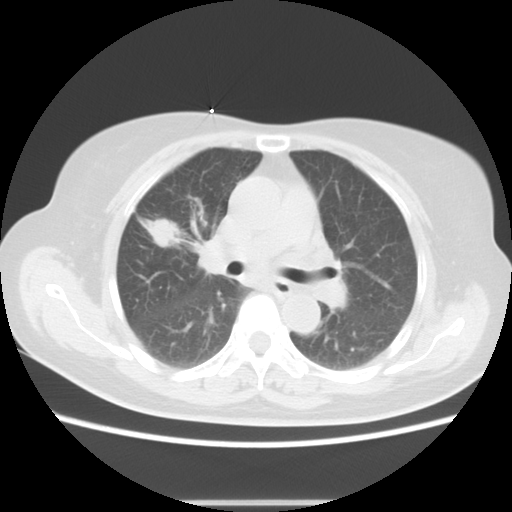
Chest CT, one axial slice; slice 7 of 17 in the series (ordered by position); lung window (W 1500 / L -600 HU); 512 × 512 image matrix. Female patient, age 57 years. Case-level facts recorded for this patient, not image findings: clinical TNM (as recorded): T1c N1 M0.
Annotated regions visible in this slice (bounding box drawn by a radiologist):
- lung tumour (recorded histology: adenocarcinoma): box from (x=145, y=215) to (x=178, y=252) px